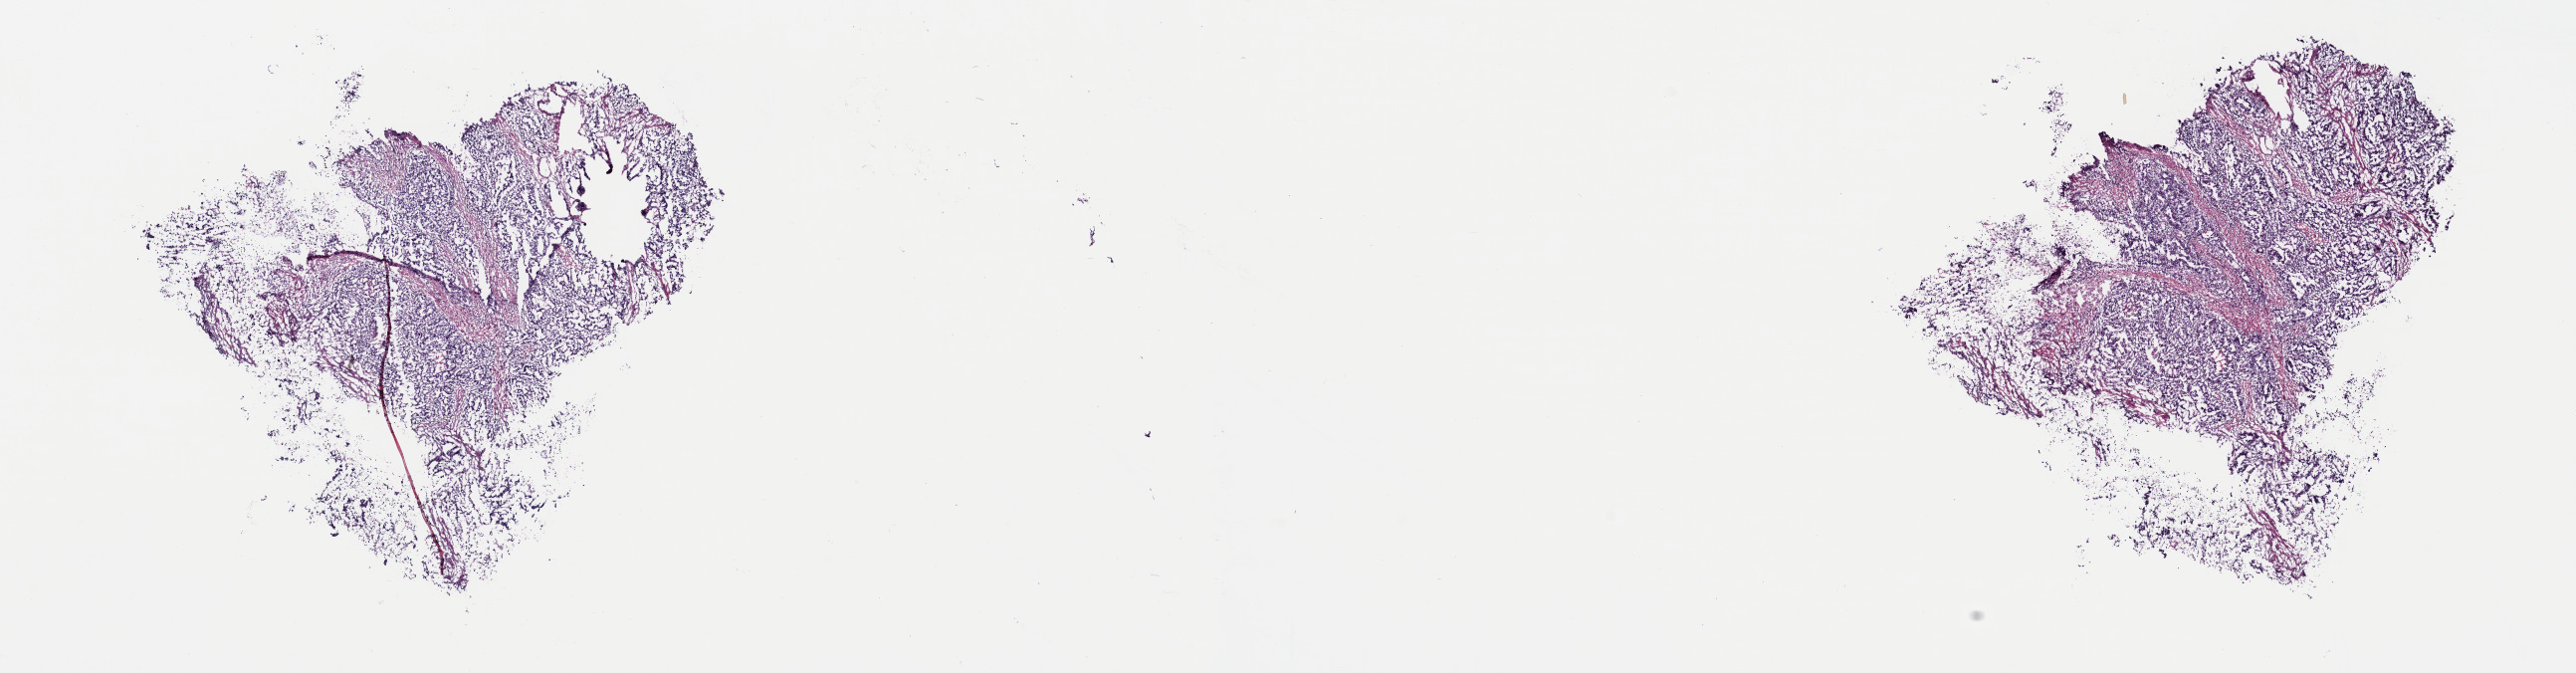
Digitized H&E-stained tissue section (whole slide) — shown as a low-resolution overview of the whole scanned area (about 20.4 x 5.3 mm, acquisition: 40x scan), frozen section, sample: primary tumour, stomach. Female, age 86 years at initial diagnosis. Histologic grade: G2 (moderately differentiated). Slide review estimates, as recorded: tumour cells 80%, tumour nuclei 85%, normal cells 0%, stromal cells 20%, necrosis 0%. Inflammatory infiltration, as recorded: lymphocyte infiltration 0%, monocyte infiltration 0%, neutrophil infiltration 0%.
- diagnosis: Carcinoma, diffuse type (gastric antrum)
- AJCC pathologic stage: IIA (7th edition)